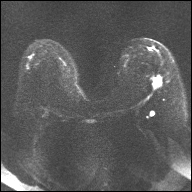
Breast MRI, one axial slice. Position 17 of 32 along the scan axis. Diffusion-weighted series; image 2 of 4 stored at this slice position (different b-values; order by instance number). 1.5 T. 4 mm slice thickness. 192 × 192 image matrix, field of view 360 × 360 mm. Female patient.
Outlined on this slice (expert manual segmentation):
- tumour on diffusion-weighted imaging: bounding box <154,80,161,88> (left, top, right, bottom; pixels)